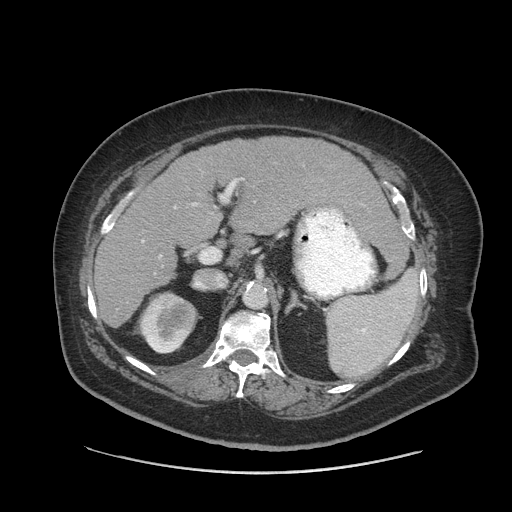
Contrast-enhanced abdominal CT (liver protocol), one axial slice. 140 kVp. Soft-tissue window (W 400 / L 40 HU). 2.5 mm slice thickness. 512 × 512 image matrix. Case-level facts recorded for this patient, not image findings: diagnosis: hepatocellular carcinoma (patient treated with transarterial chemoembolisation; whether this scan precedes or follows treatment is not stated here); TNM stage (as recorded): Stage-I; Child-Pugh class: A; tumour differentiation: well differentiated.
Structures marked on this image (semi-automatic segmentation, software-assisted and operator-edited):
- liver parenchyma outside the tumour (the mass and vessels are separate outlines, so this box may not span the whole liver): bounding box [x1, y1, x2, y2] px = [94, 136, 388, 328]
- liver vessels: [142, 179, 237, 243]